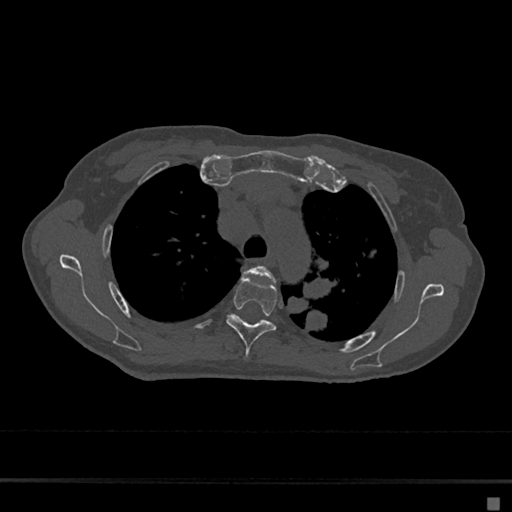
CT including the spine, one axial slice; slice 500 of 797 in the series (ordered by position); 120 kVp; bone window (W 1800 / L 400 HU); 0.5 mm slice thickness; 512 × 512 image matrix. Female patient, age 68 years. From the clinical record (not read from this slice): primary cancer: renal.
Structures marked on this image (semi-automatically segmented with operator editing):
- T3 vertebra: box from (x=243, y=266) to (x=273, y=279) px
- T4 vertebra: (x=226, y=277)–(x=277, y=359)
- T5 vertebra: (x=234, y=317)–(x=239, y=319)